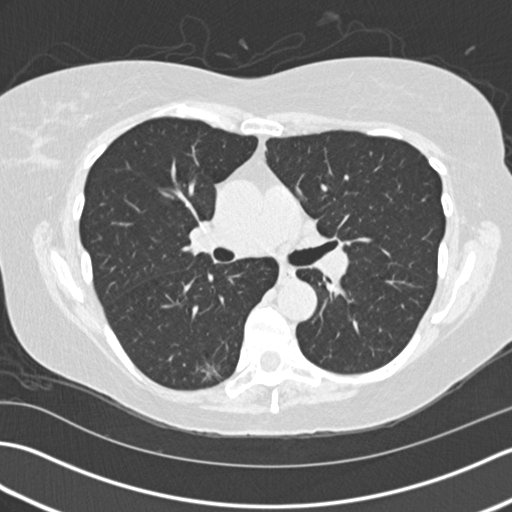
Axial slice from a low-dose chest CT screening exam; third screening round (two years after baseline); lung window (W 1500 / L -600 HU); 2 mm slice thickness; 512 × 512 image matrix. Female, age 60 years at enrolment. Former smoker at enrolment.
- Expert-annotated lung lesion, box from (x=189, y=348) to (x=240, y=389) px.
- The screening reader recorded 3 non-calcified nodules or masses ≥4 mm on this exam (right lower lobe, right middle lobe, right middle lobe); which of them this box marks is not recorded.
- Official screen result: positive, other.
- Later outcome: lung cancer diagnosed 68 days after this screen — acinar cell carcinoma, right lower lobe, moderately differentiated (G2), stage IA (AJCC 6th edition), 10 mm at pathology.